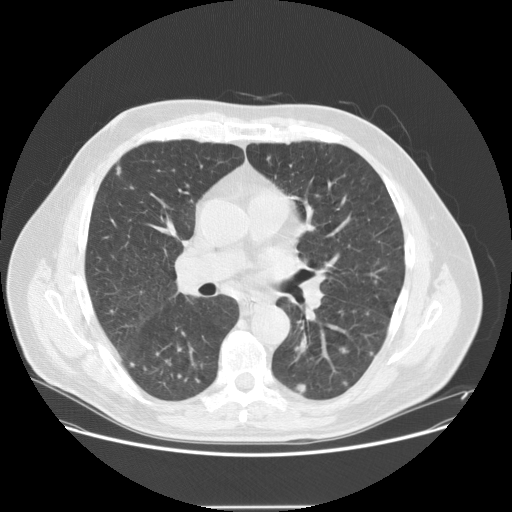
Low-dose screening chest CT, one axial slice; slice 81 of 143 in the series (ordered by position); 120 kVp; lung window (W 1500 / L -600 HU); 2.5 mm slice thickness; 512 × 512 image matrix, field of view 400 × 400 mm.
Structures marked on this image (outlined manually by an expert reader):
- lesion 5 (tumor): bounding box <296,384,306,392> (left, top, right, bottom; pixels)